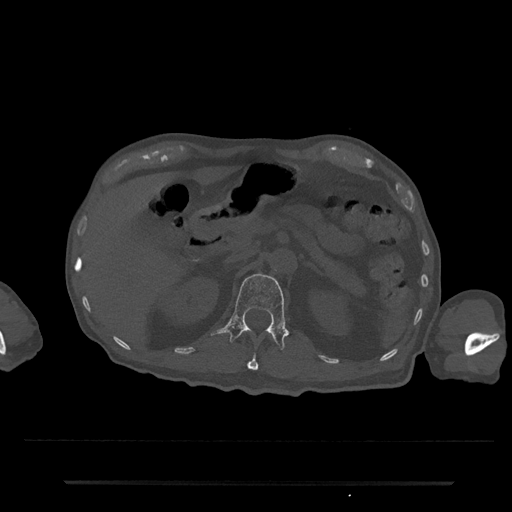
CT including the spine, one axial slice. Position 147 of 797 along the scan axis. Reconstruction kernel Br40s/3. 120 kVp. Bone window (W 1800 / L 400 HU). 0.5 mm slice thickness. 512 × 512 image matrix. Patient: male, 74 years. Case-level facts recorded for this patient, not image findings: primary cancer: prostate.
Outlined on this slice (semi-automatically segmented with operator editing):
- L1 vertebra: bounding box [x1, y1, x2, y2] px = [212, 273, 288, 350]
- T12 vertebra: [247, 355, 259, 371]